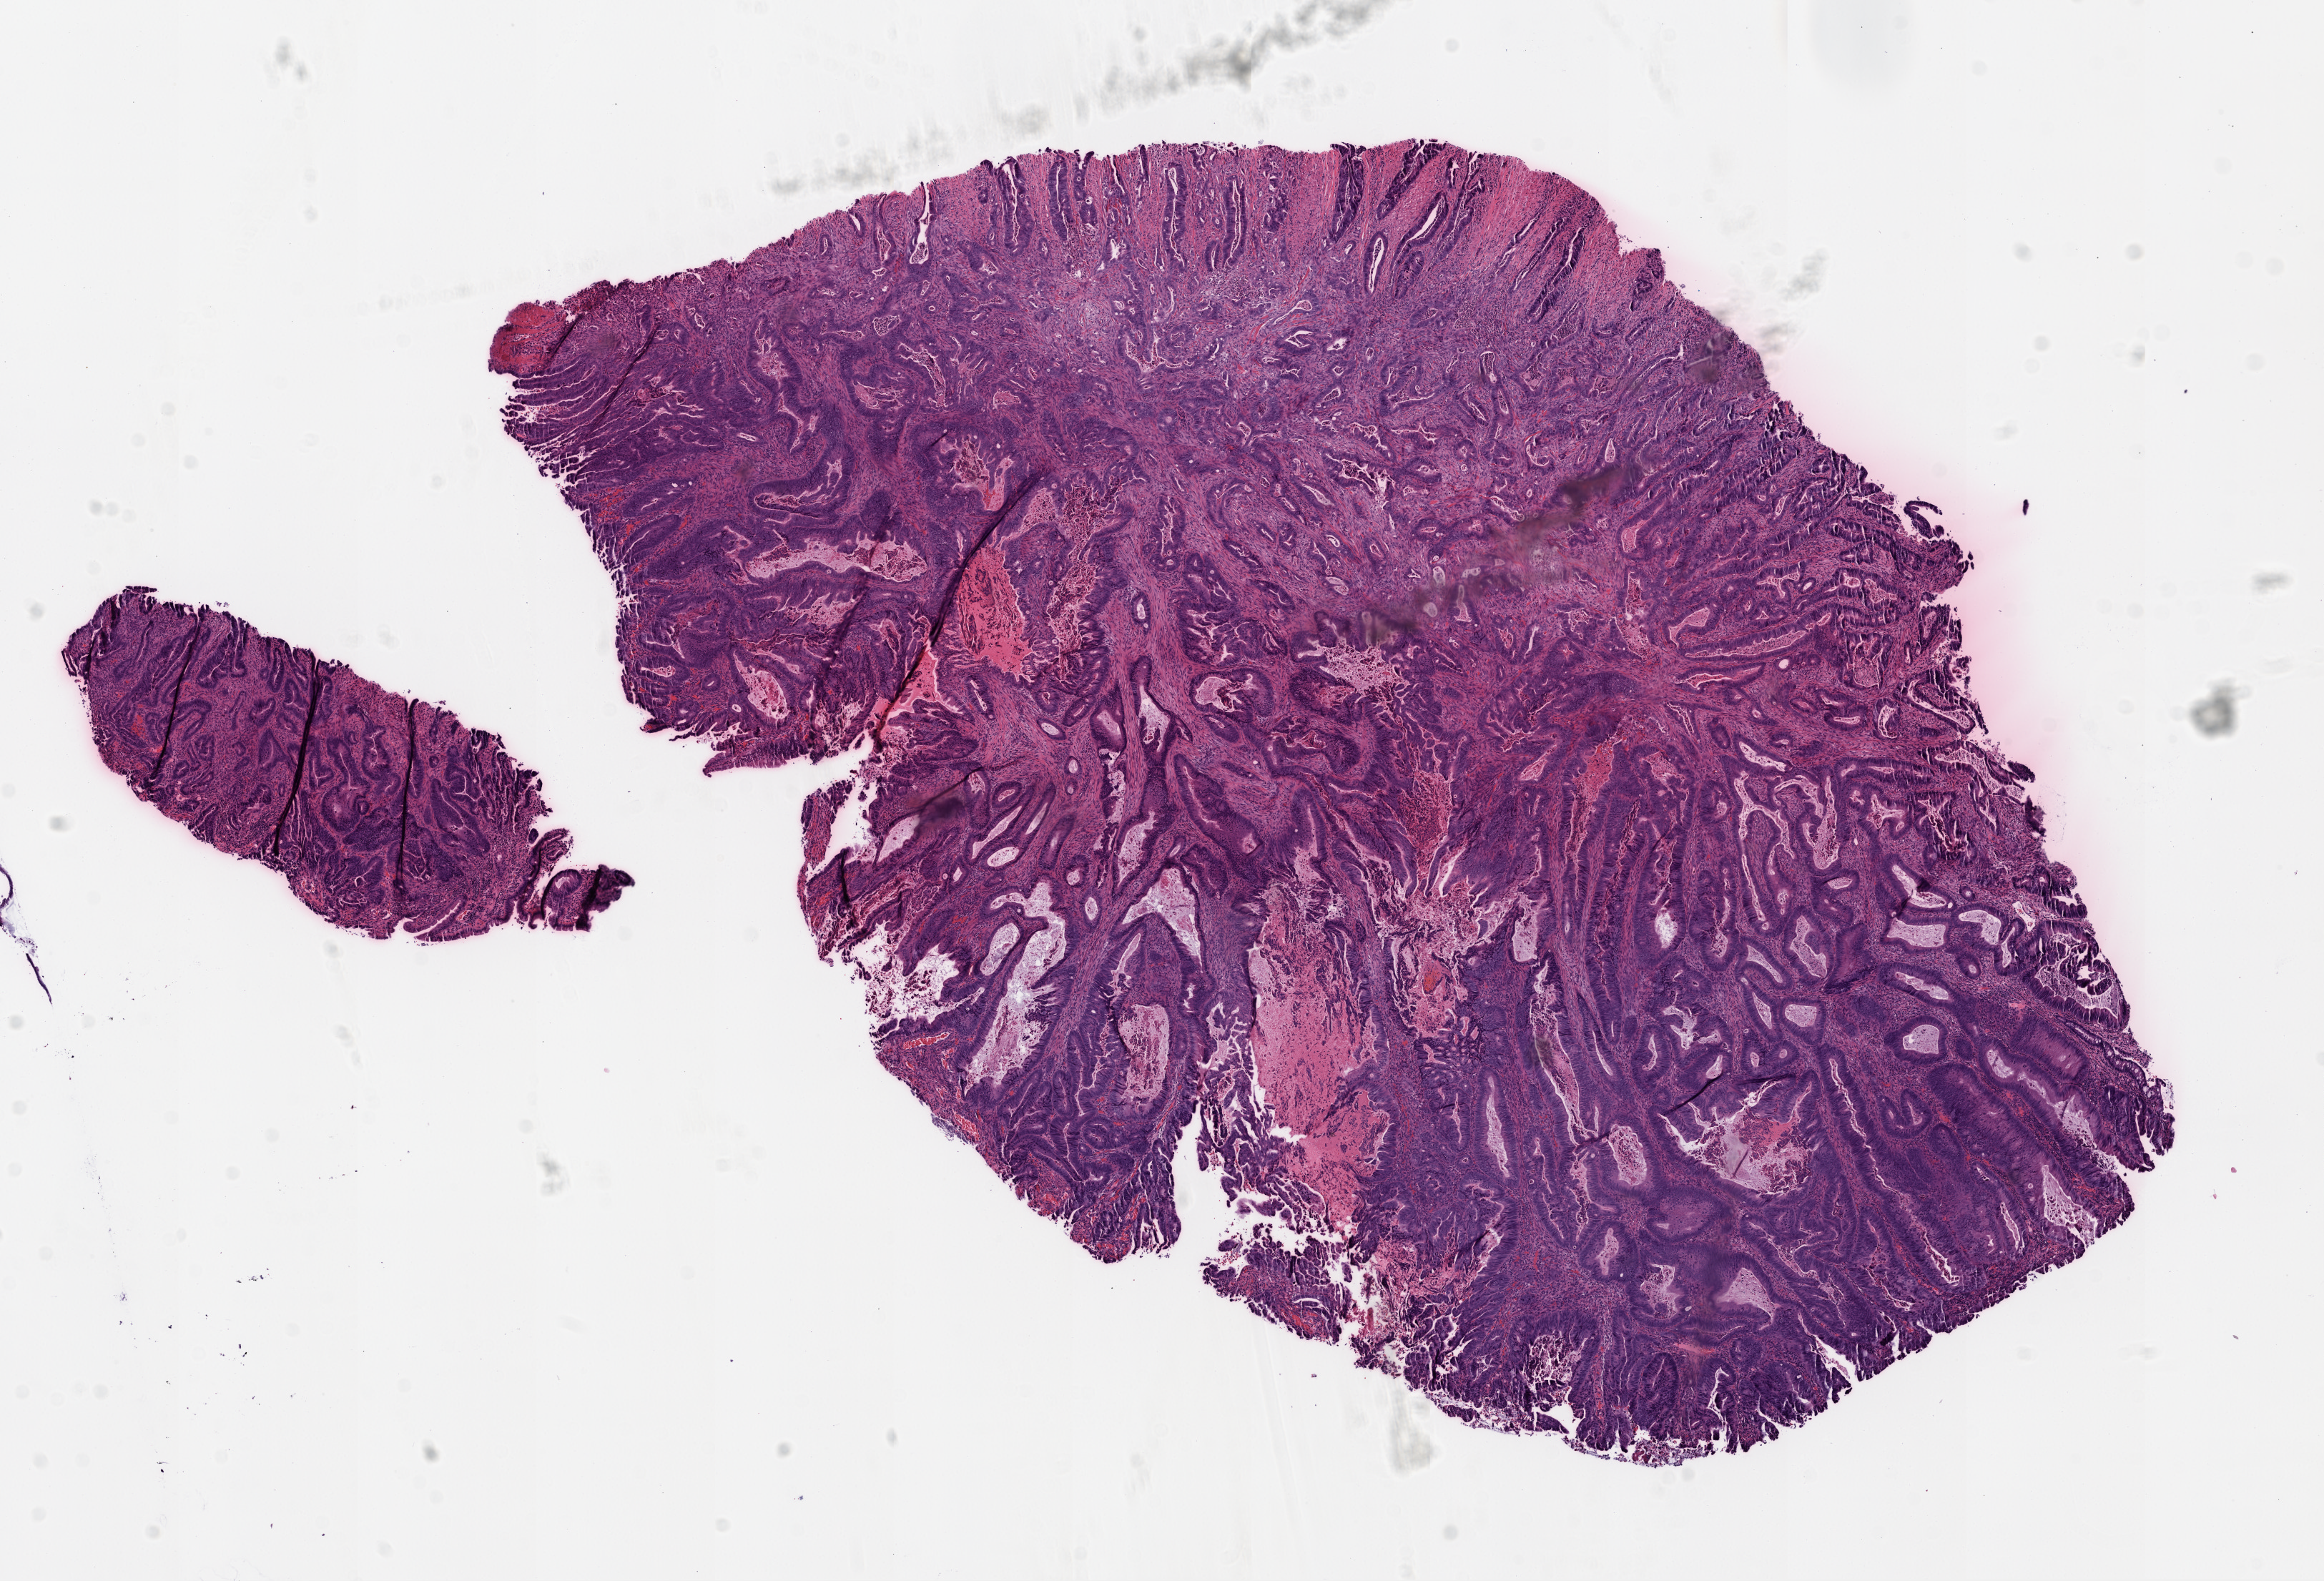
Digitized H&E-stained tissue section (whole slide), low-resolution overview of the scanned area, about 13.0 x 8.9 mm (acquisition: 20x scan); frozen section from the top of the tissue portion; colon, primary tumour sample. Female patient; age at initial diagnosis 53 years. Pathologist review of this section (percent, as recorded): tumour cells 65%, tumour nuclei 75%, normal cells 0%, stromal cells 20%, necrosis 15%.
AJCC pathologic stage: IIIC. Diagnosis: Adenocarcinoma, NOS (sigmoid colon). TNM: T3 N2 M0.